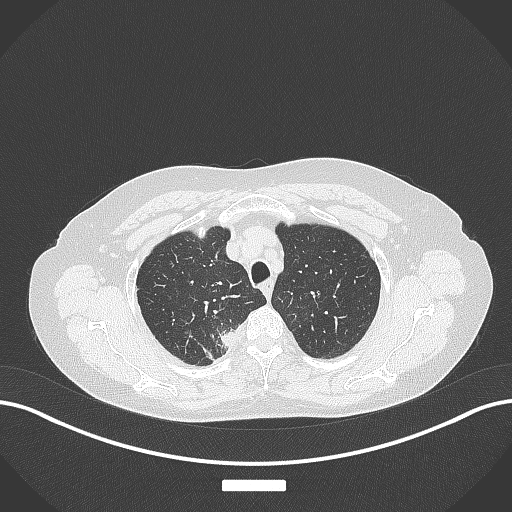
Chest CT, one axial slice. Position 322 of 357 along the scan axis. Reconstruction kernel B70f. 120 kVp. Lung window (W 1500 / L -600 HU). 512 × 512 image matrix. Patient: female, 62 years. From the clinical record (not read from this slice): clinical TNM (as recorded): T1c N1 M0.
Outlined on this slice (rectangle marked by the reading radiologist):
- lung tumour (recorded histology: squamous cell carcinoma): box from (x=213, y=322) to (x=240, y=350) px